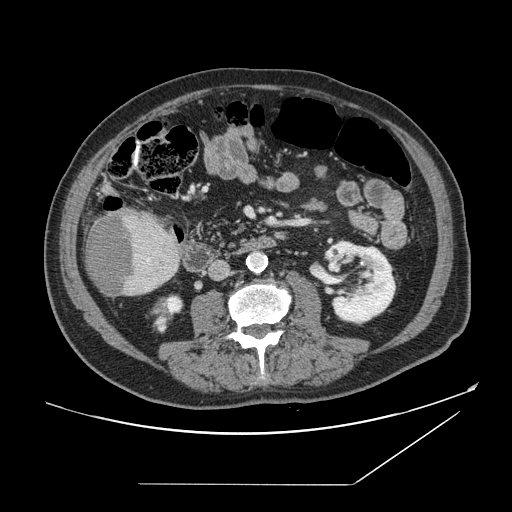
Contrast-enhanced abdominal CT, one axial slice. Slice 42 of 166 in the series (ordered by position). 120 kVp. Soft-tissue window (W 400 / L 40 HU). 512 × 512 image matrix, field of view 416 × 416 mm. Male patient, age 80 years. From the clinical record (not read from this slice): diagnosis: colorectal cancer liver metastases, imaged before liver resection; multiple liver metastases: no; largest metastasis: 2.2 cm; disease in both lobes: no.
Outlined on this slice (manually delineated by an expert):
- liver: box from (x=86, y=209) to (x=180, y=297) px
- liver metastasis: (x=88, y=212)–(x=135, y=296)